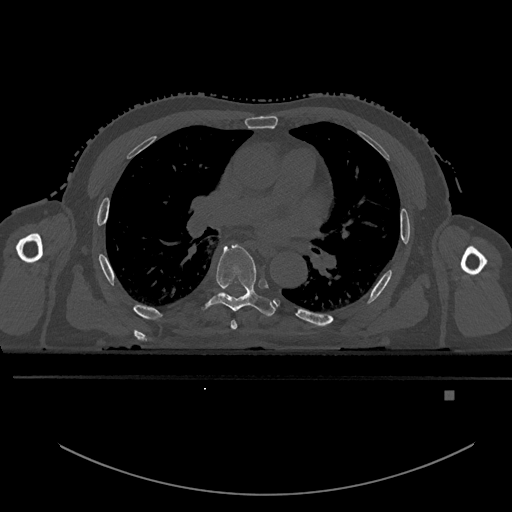
CT including the spine, one axial slice; slice 311 of 969 in the series (ordered by position); bone window (W 1800 / L 400 HU); 512 × 512 image matrix, field of view 456 × 456 mm. Patient: male, 82 years. From the clinical record (not read from this slice): primary cancer: prostate; vertebrae with lytic lesions (as recorded): T11, T9, T8, T2.
Annotated regions visible in this slice (semi-automatically segmented with operator editing):
- T5 vertebra: box from (x=230, y=320) to (x=237, y=330) px
- T6 vertebra: (x=200, y=245)–(x=277, y=317)